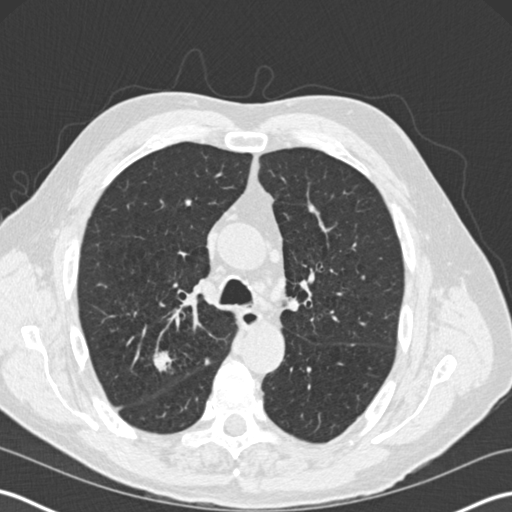
Chest CT (low-dose screening protocol), one axial image; third annual screen; lung window (W 1500 / L -600 HU); 2 mm slice thickness; standard (soft-tissue) reconstruction kernel (B30f); slice 72 of 199 in the series; 512 × 512 image matrix, field of view 350 × 350 mm. Male participant, aged 65 years at enrolment.
Expert reader's lesion annotation, bounding box [x1, y1, x2, y2] px = [141, 347, 181, 381]. The screening reader recorded 6 non-calcified nodules or masses ≥4 mm on this exam (right upper lobe, left upper lobe, left upper lobe, left upper lobe, right upper lobe); which of them this box marks is not recorded. Participant outcome: lung cancer diagnosed 78 days after this screen — adenocarcinoma, NOS, right upper lobe, moderately differentiated (G2), stage IA (AJCC 6th edition), 16 mm at pathology.